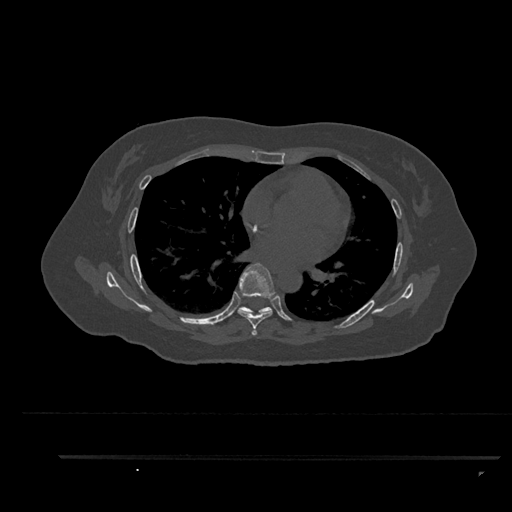
CT including the spine, one axial slice. Slice 540 of 797 in the series (ordered by position). Reconstruction kernel Br40s/3. 120 kVp. Bone window (W 1800 / L 400 HU). 0.5 mm slice thickness. 512 × 512 image matrix. Female patient, age 44 years. From the clinical record (not read from this slice): primary cancer: renal.
Outlined on this slice (semi-automatically segmented with operator editing):
- T6 vertebra: bounding box [x1, y1, x2, y2] px = [238, 263, 276, 336]
- T7 vertebra: [238, 307, 272, 315]